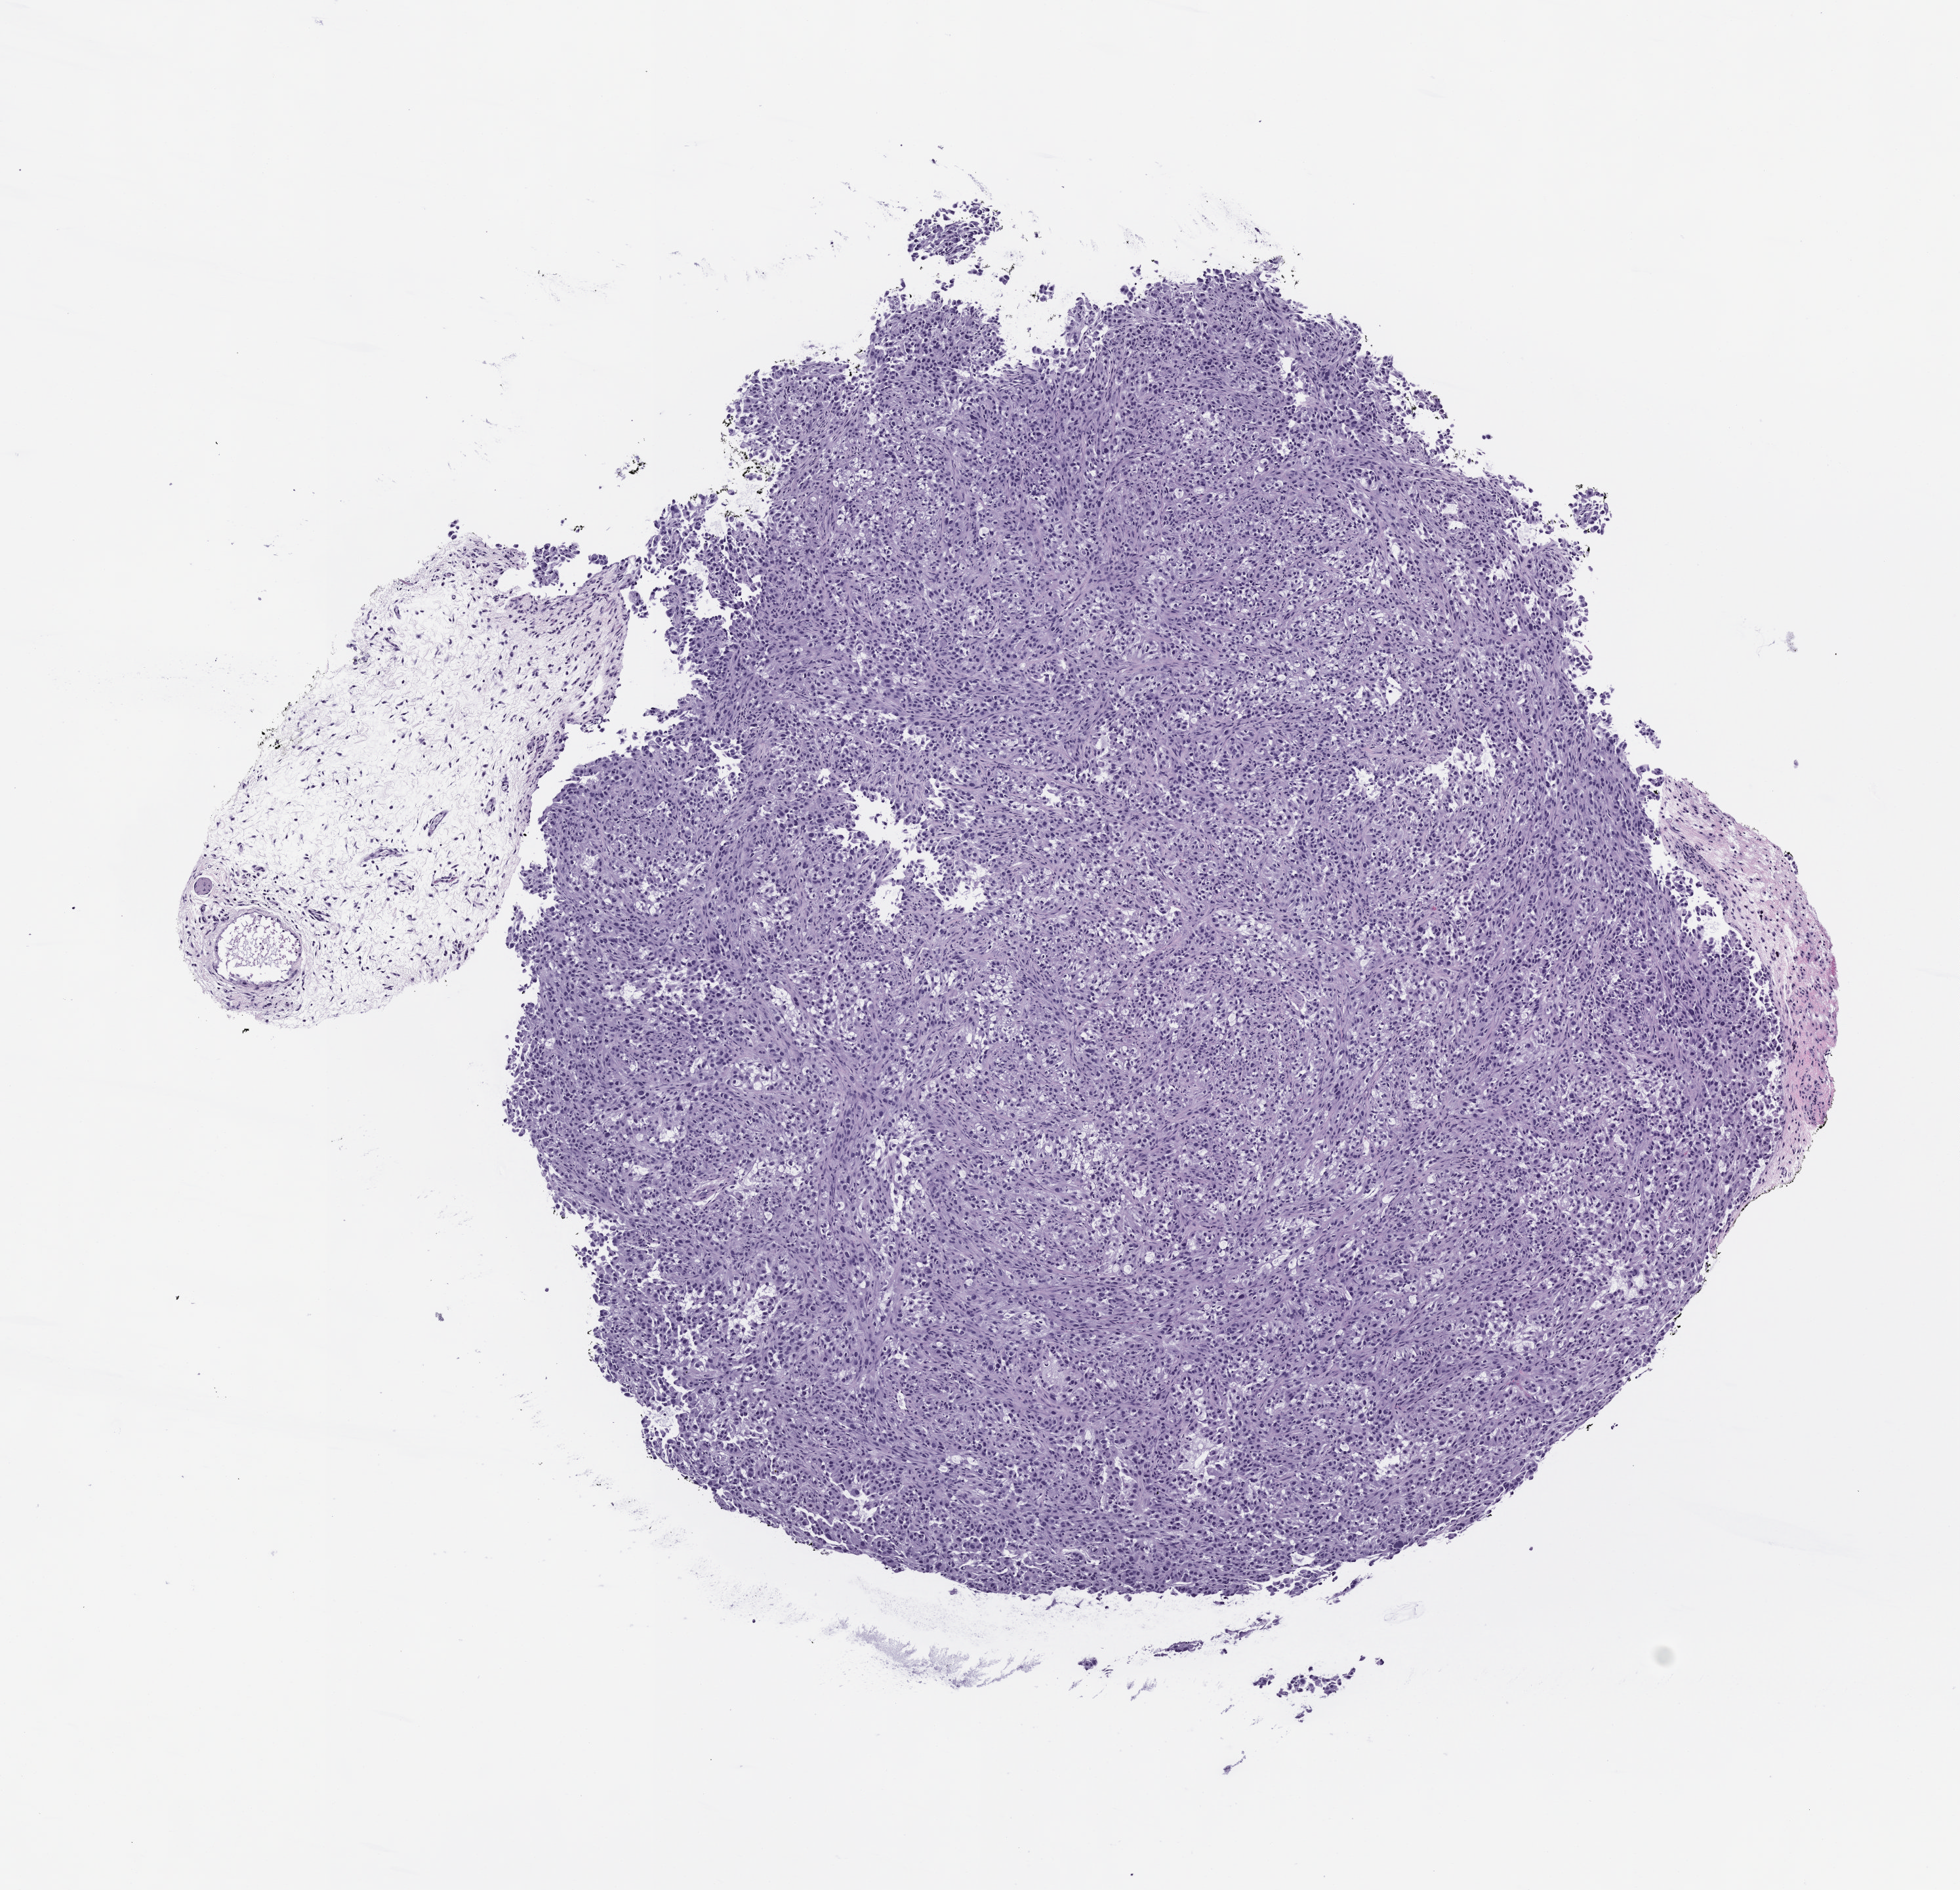
Whole-slide image, hematoxylin and eosin (H&E): patient-derived xenograft (human tumor grown in a mouse), passage 3, whole scanned area (about 6.0 x 5.8 mm) shown as a low-resolution overview; formalin-fixed paraffin-embedded section; tumor site category: genitourinary tract.
Originating patient diagnosis: Renal Cell Carcinoma, Not Otherwise Specified.